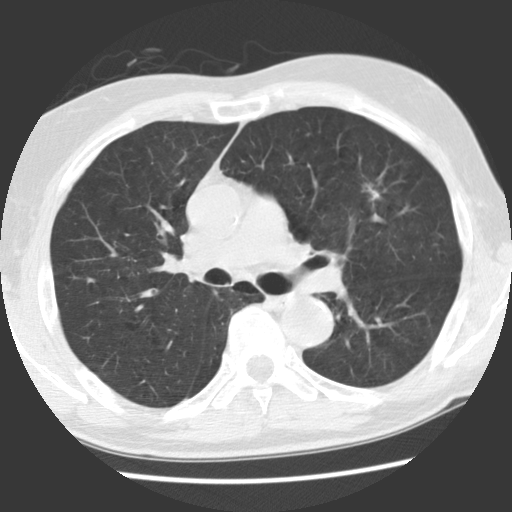
Chest CT (low-dose screening protocol), one axial image; first (baseline) screen; lung window (W 1500 / L -600 HU); standard (soft-tissue) reconstruction kernel (STANDARD); 140 kVp; slice 79 of 131 in the series; 512 × 512 image matrix, field of view 320 × 320 mm. Male participant, aged 70 years at enrolment. Current smoker at enrolment.
Lesion marked by an expert reader, box from (x=346, y=175) to (x=401, y=222) px. The screening reader recorded 2 non-calcified nodules or masses ≥4 mm on this exam (left upper lobe, right lower lobe); which of them this box marks is not recorded. Later outcome: lung cancer diagnosed 879 days after this screen (after the third annual screen) — adenocarcinoma, NOS, left upper lobe, moderately differentiated (G2), stage IIIA (AJCC 6th edition), 17 mm at pathology.